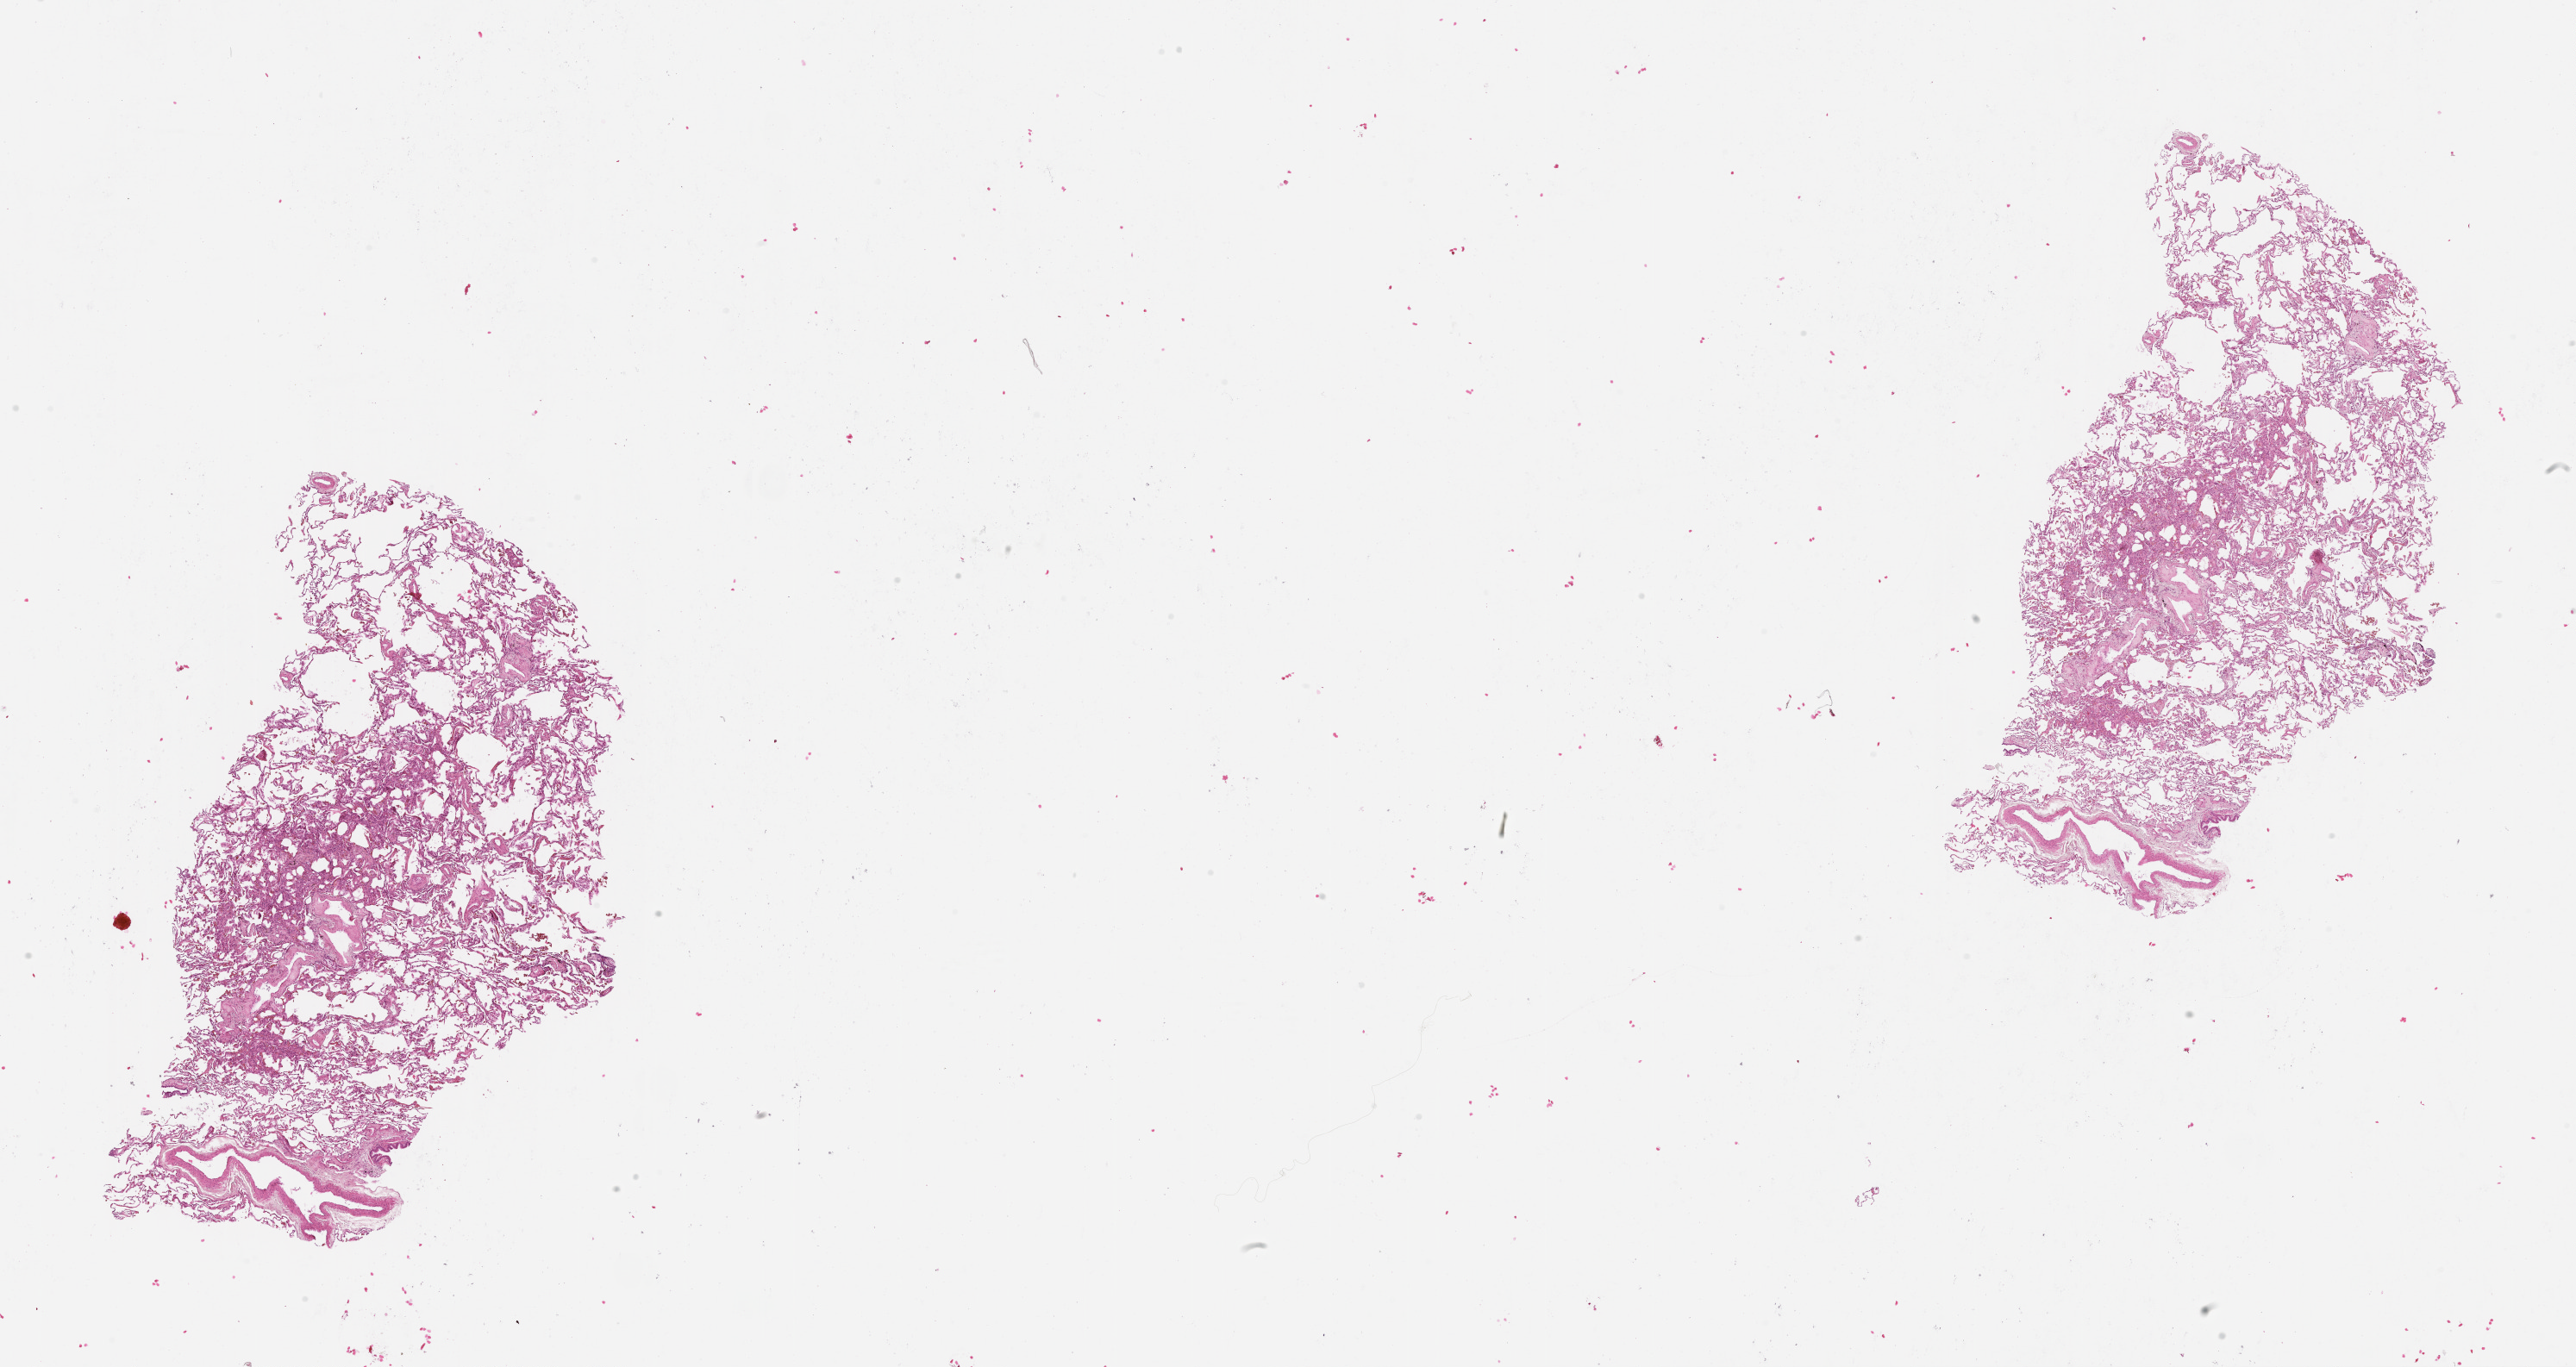
Digitized H&E tissue section (whole slide), shown as a low-resolution overview of the whole scanned area (about 24.1 x 12.8 mm, acquisition: 20x scan). Normal (non-tumour) tissue sample, lung. Patient: female, age 70 years.
• this section: normal (non-tumour) tissue from the same patient
• patient diagnosis (cohort enrolment): squamous cell carcinoma (lung)